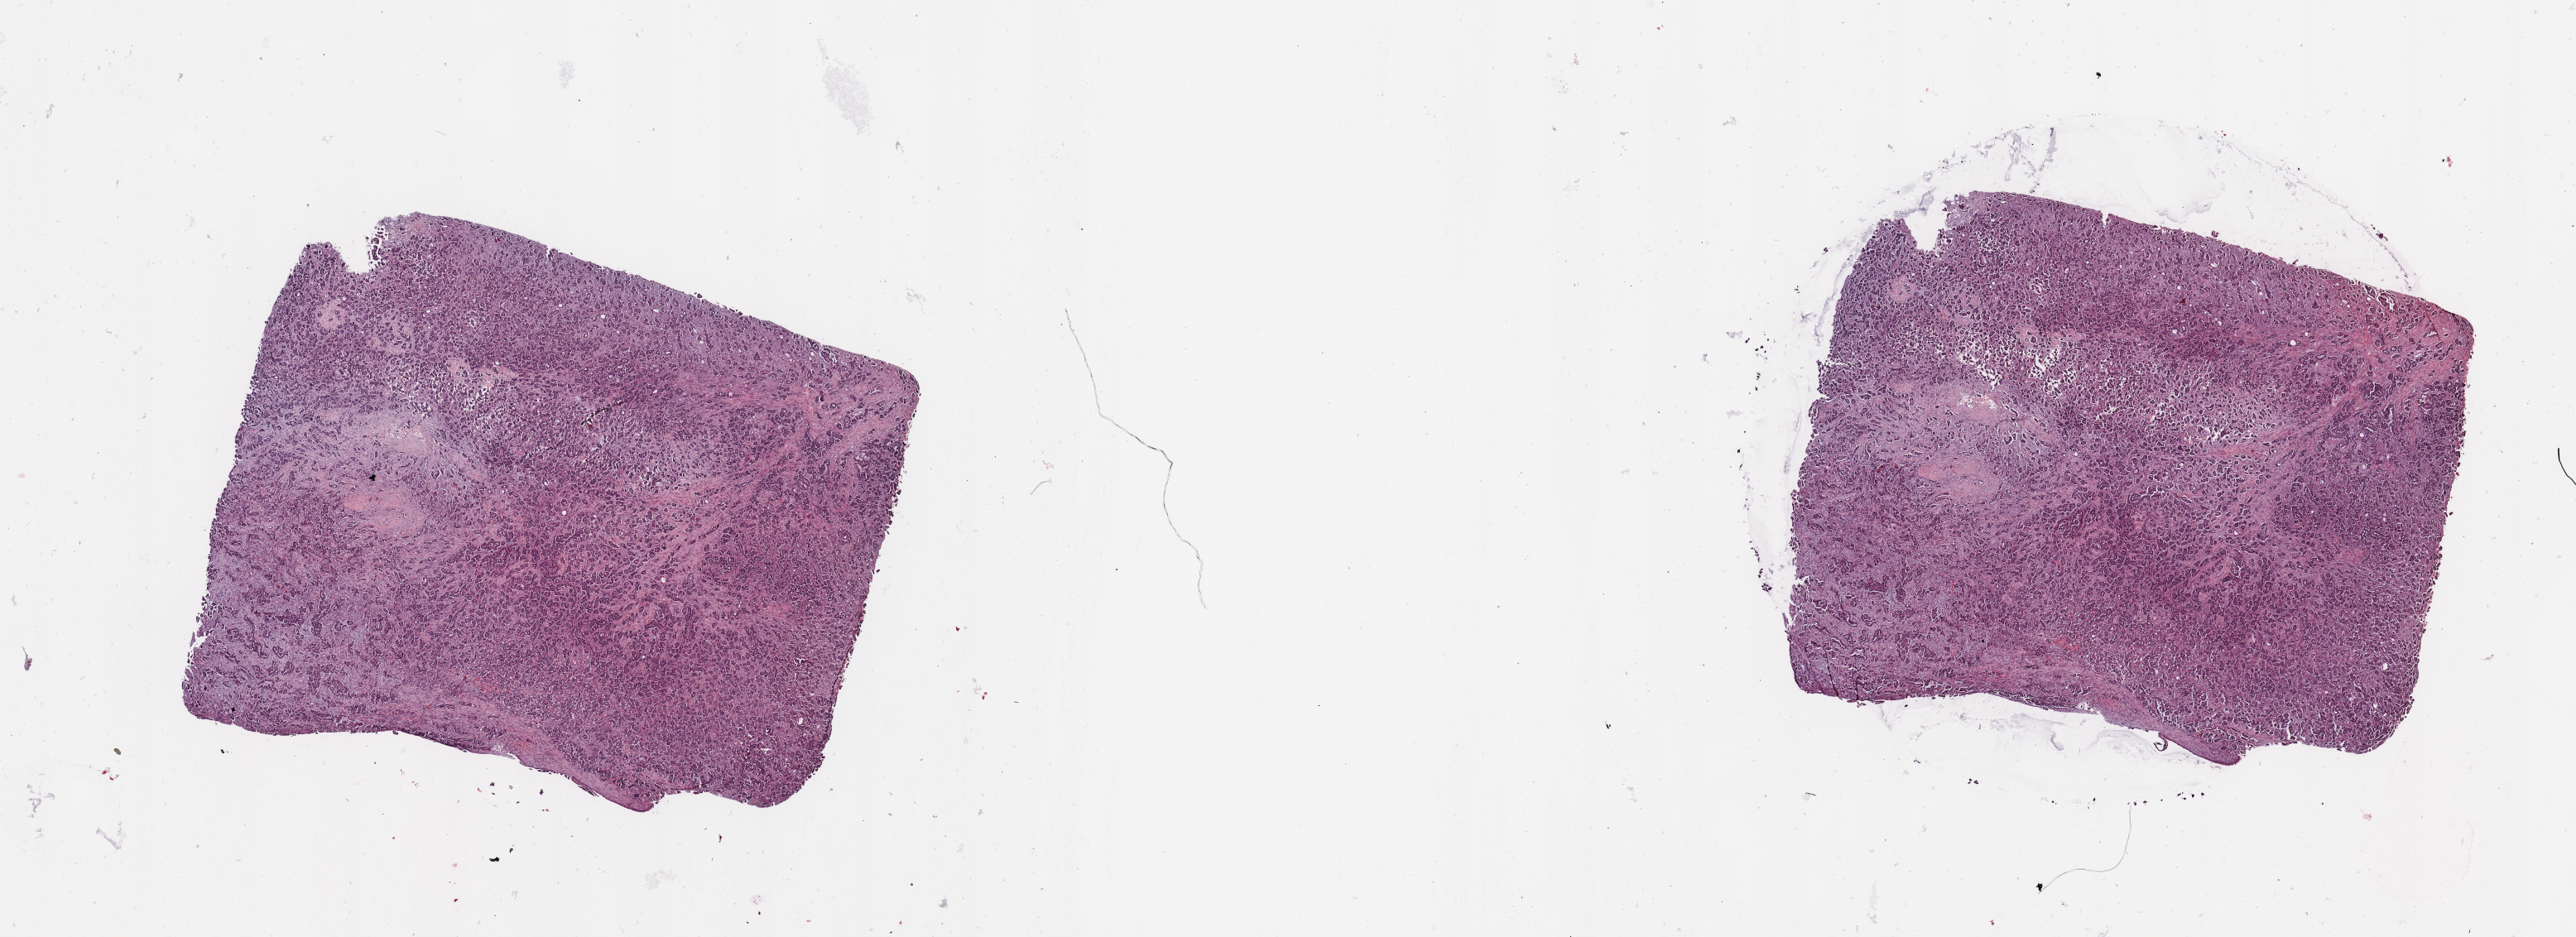
Digitized H&E-stained tissue section (whole slide), a low-resolution overview of the entire scanned area, about 24.6 x 9.0 mm, tumour tissue sample, sampled site: lung. Patient: male, age 39 years. Histologic grade: G2 (moderately differentiated). Slide review estimates, as recorded: tumour nuclei 75%, necrosis 2%.
AJCC pathologic stage: IIIA. Diagnosis: Adenocarcinoma, NOS.